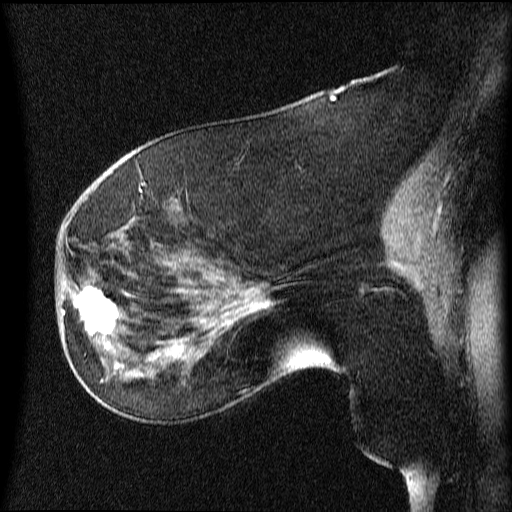
Breast MRI (dynamic contrast-enhanced), one sagittal slice. Slice 29 of 64 in the series (ordered by position). Dynamic contrast-enhanced series, image 2 of 4 at this slice position (ordered by acquisition). 1.5 T. TE 4.2 ms, TR 9 ms. 2 mm slice thickness. 512 × 512 image matrix, field of view 200 × 200 mm. Female patient, age 63 years.
Structures marked on this image (semi-automatic segmentation, software-assisted and operator-edited):
- analysis volume of interest (the breast-tissue region the enhancement analysis was run in; not a lesion): bounding box (x1, y1, x2, y2) in pixels: (66, 272, 131, 353)
- tumour enhancement mask (voxels above the 70 % enhancement threshold inside the analysis volume of interest): (76, 286, 118, 349)